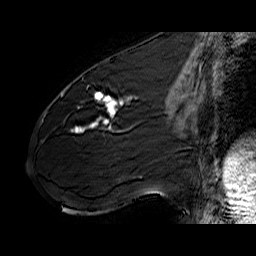
Breast MRI (dynamic contrast-enhanced), one sagittal slice; position 27 of 60 along the scan axis; dynamic contrast-enhanced series, time point 2 of 6 at this slice position (early post-contrast); 1.5 T; TE 6.4 ms, TR 32.9 ms; 256 × 256 image matrix. Female patient. Case-level facts recorded for this patient, not image findings: setting: breast cancer imaged before/during neoadjuvant chemotherapy; receptor status: HER2-positive.
Annotated regions visible in this slice (semi-automatically segmented with operator editing):
- analysis volume of interest (the breast-tissue region the enhancement analysis was run in; not a lesion): bounding box <61,77,141,142> (left, top, right, bottom; pixels)
- tumour enhancement mask (voxels above the 100 % enhancement threshold inside the analysis volume of interest): <71,92,132,133>